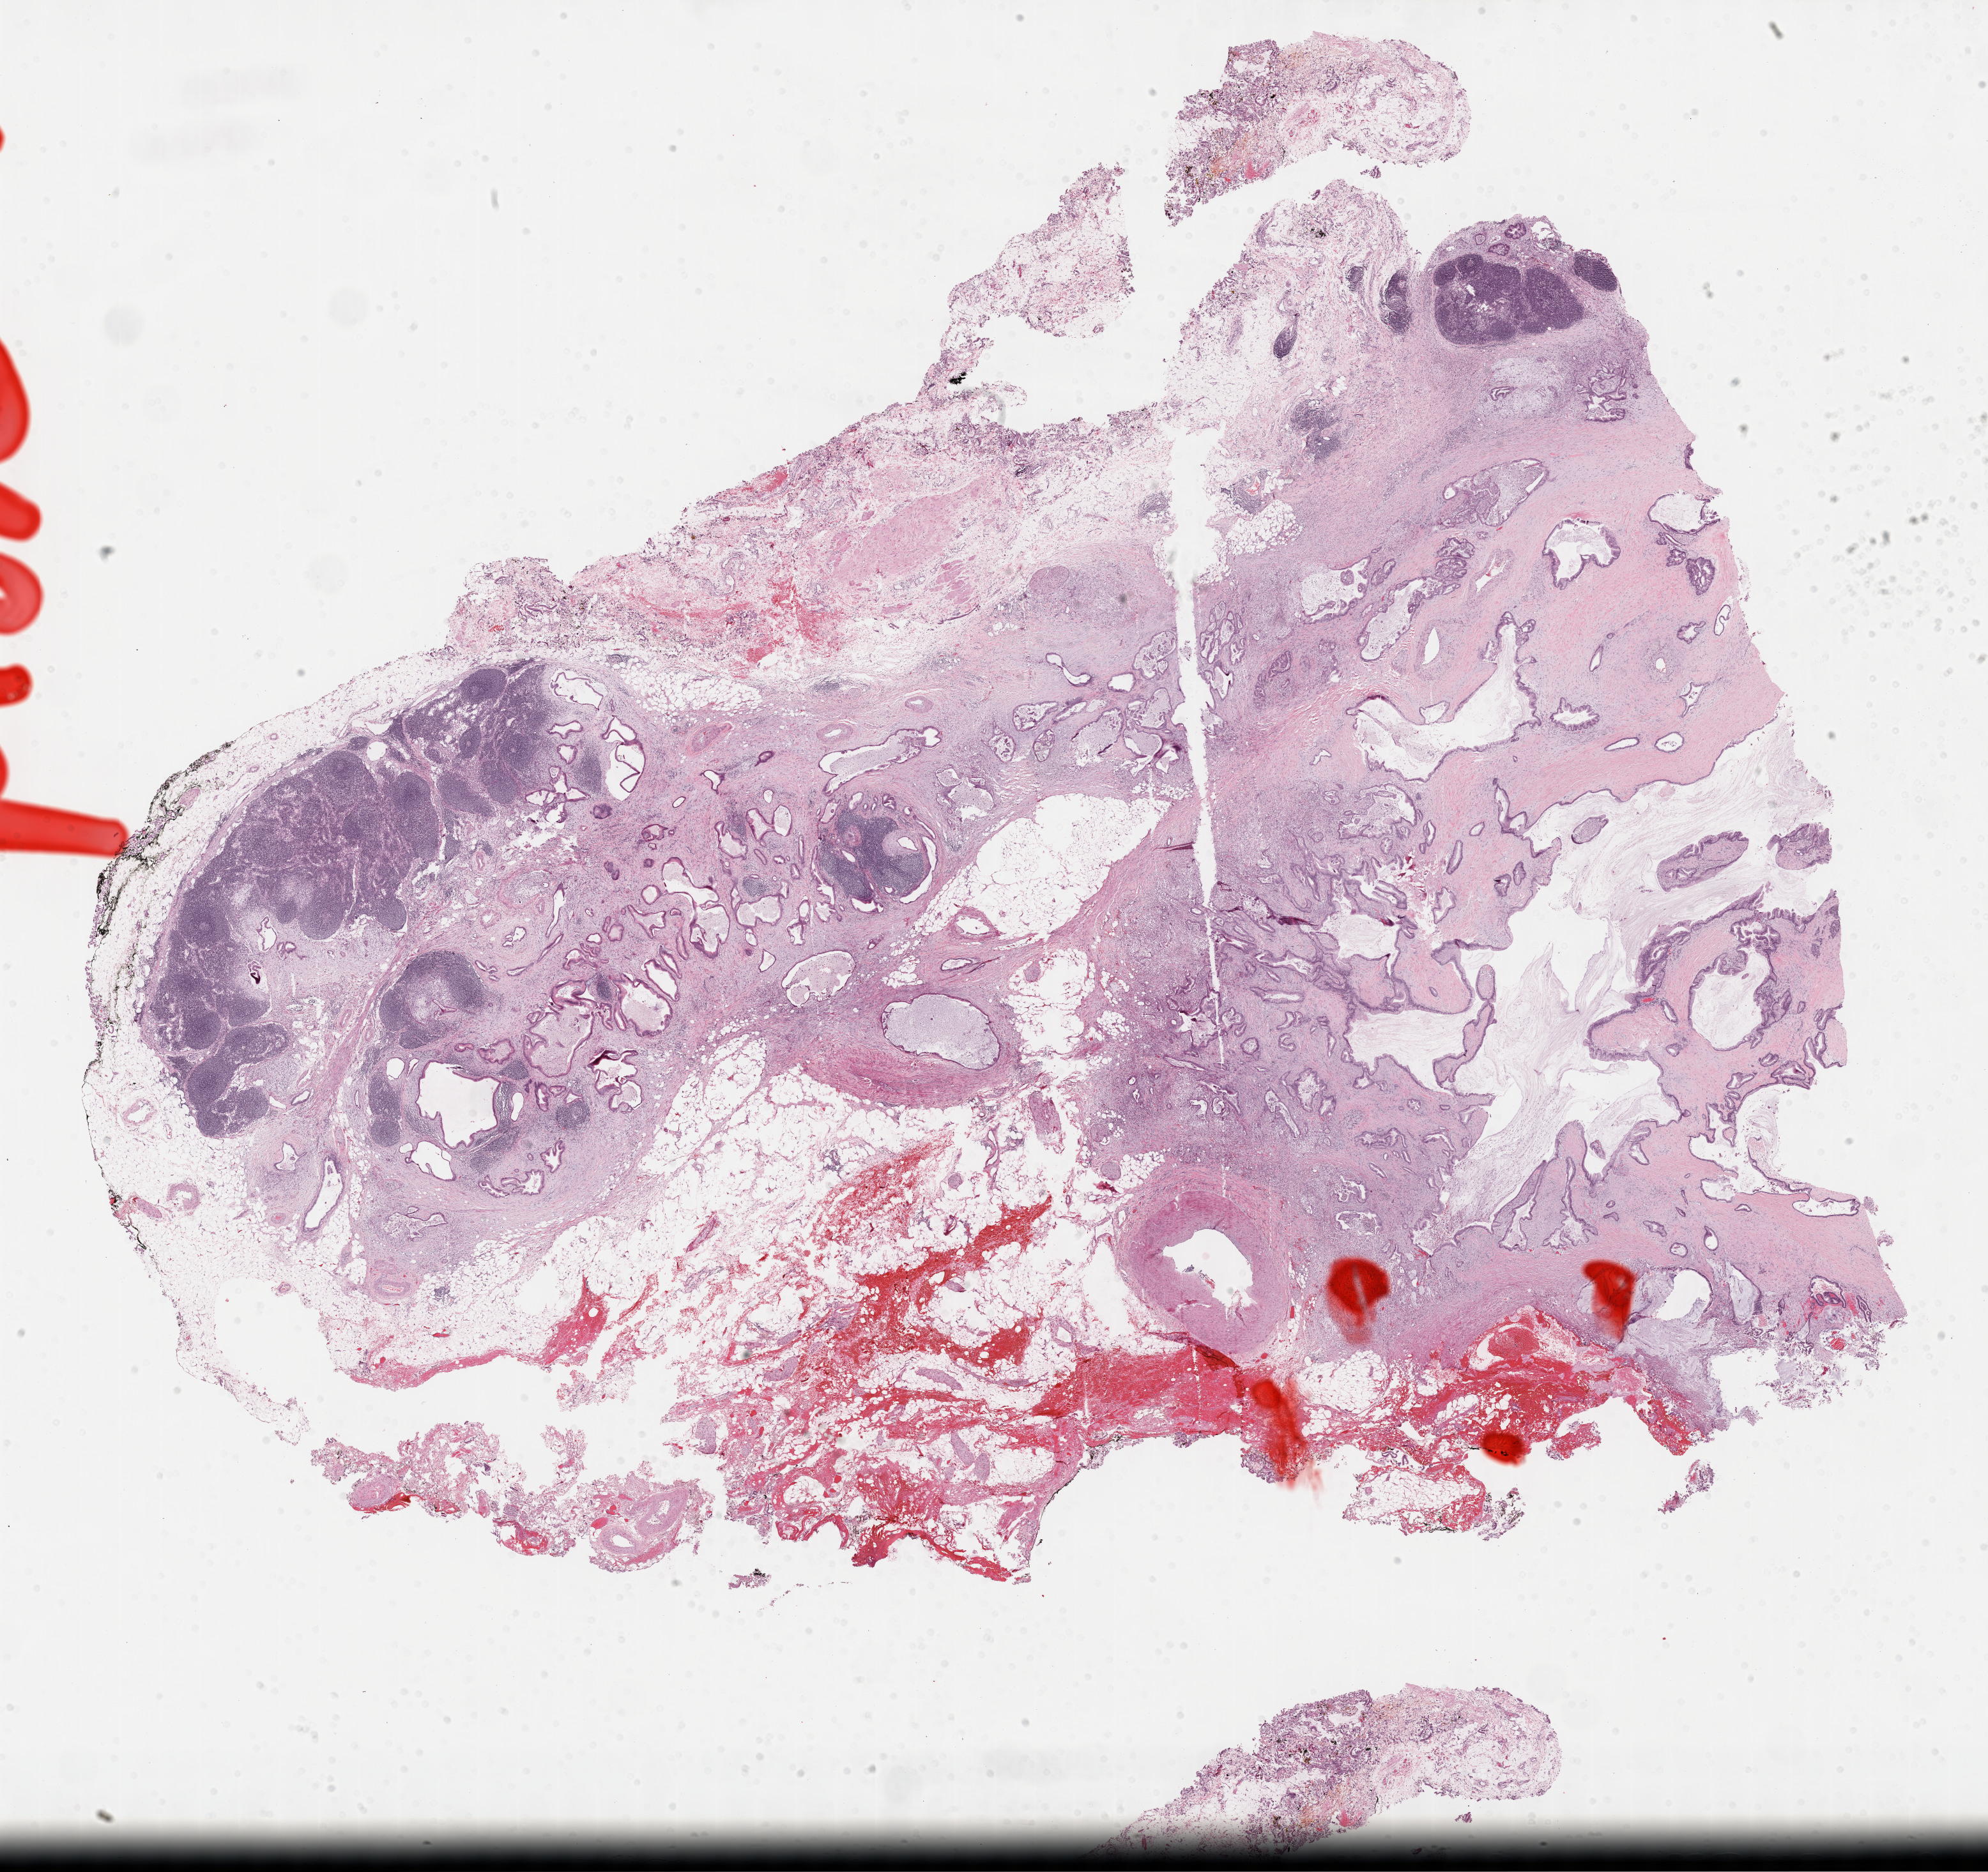
Whole-slide histology image, Hematoxylin and eosin (H&E) stained, low-resolution overview of the scanned area, about 25.2 x 23.7 mm (acquisition: 40x scan), formalin-fixed paraffin-embedded (FFPE) diagnostic section, sample: primary tumour, pancreas. Patient: female, age at initial diagnosis 64 years.
Pathologic diagnosis: Infiltrating duct carcinoma, NOS (head of pancreas).